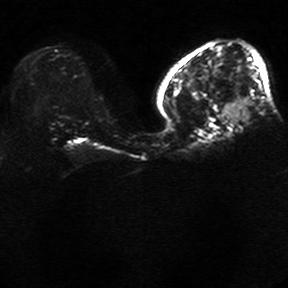
Breast MRI, one axial slice. Slice 12 of 34 in the series (ordered by position). Diffusion-weighted series; image 2 of 4 stored at this slice position (different b-values; order by instance number). 1.5 T. 288 × 288 image matrix, field of view 340 × 340 mm. Female patient.
Structures marked on this image (outlined manually by an expert reader):
- tumour on diffusion-weighted imaging: box from (x=222, y=100) to (x=248, y=124) px